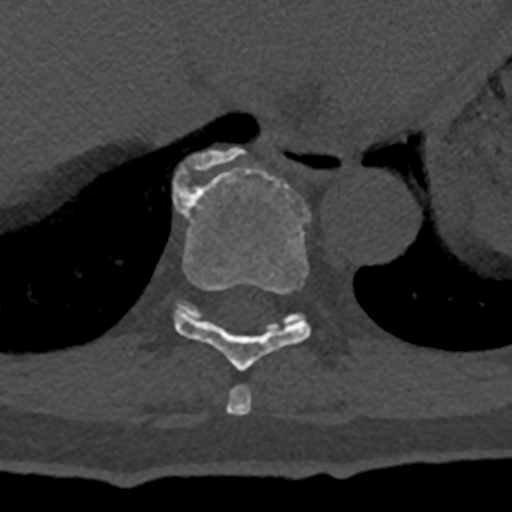
CT including the spine, one axial slice. Slice 645 of 797 in the series (ordered by position). Bone window (W 1800 / L 400 HU). 0.5 mm slice thickness. 512 × 512 image matrix, field of view 160 × 160 mm. Patient: male, 74 years. From the clinical record (not read from this slice): primary cancer: renal; vertebrae with lytic lesions (as recorded): T10, L1, L2, L3, L4, L5.
Structures marked on this image (semi-automatic segmentation, software-assisted and operator-edited):
- T10 vertebra: bounding box [x1, y1, x2, y2] px = [173, 147, 301, 327]
- T8 vertebra: [226, 385, 252, 415]
- T9 vertebra: [174, 168, 311, 371]